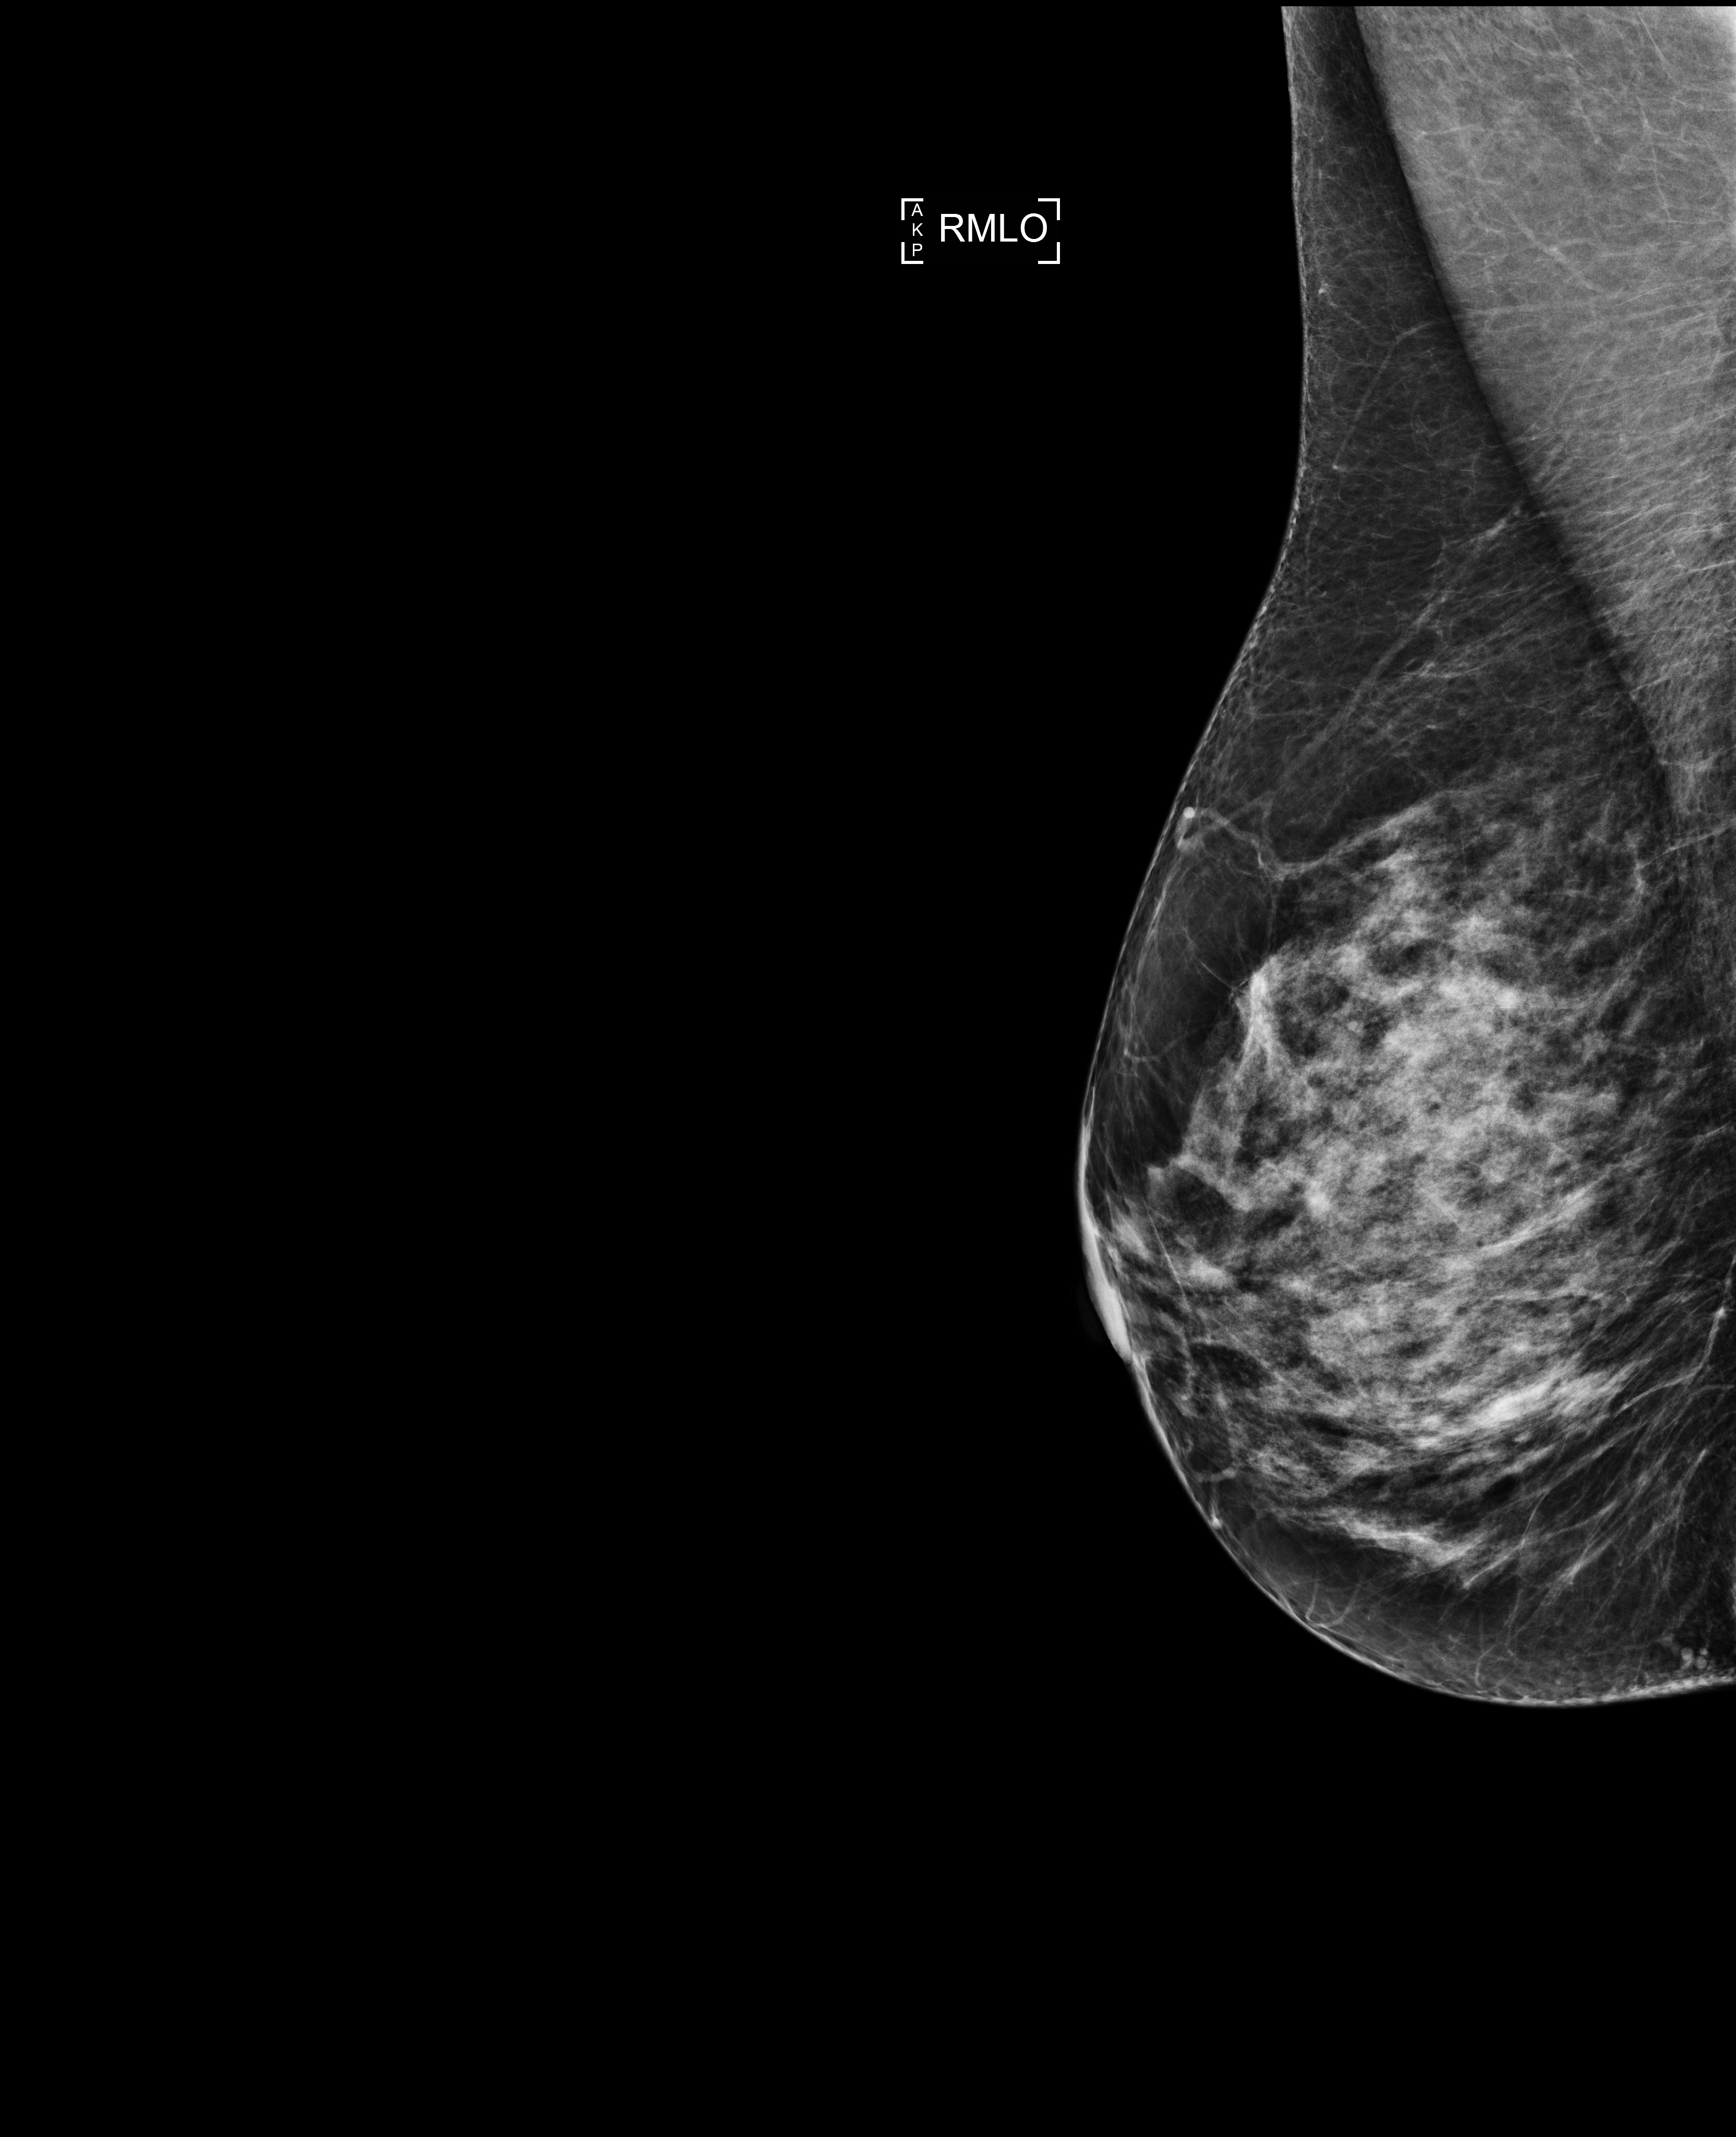
Screening examination. Patient aged 52 years (female).
Image type: full-field digital mammogram. Breast: right. Projection: mediolateral oblique (MLO) view.